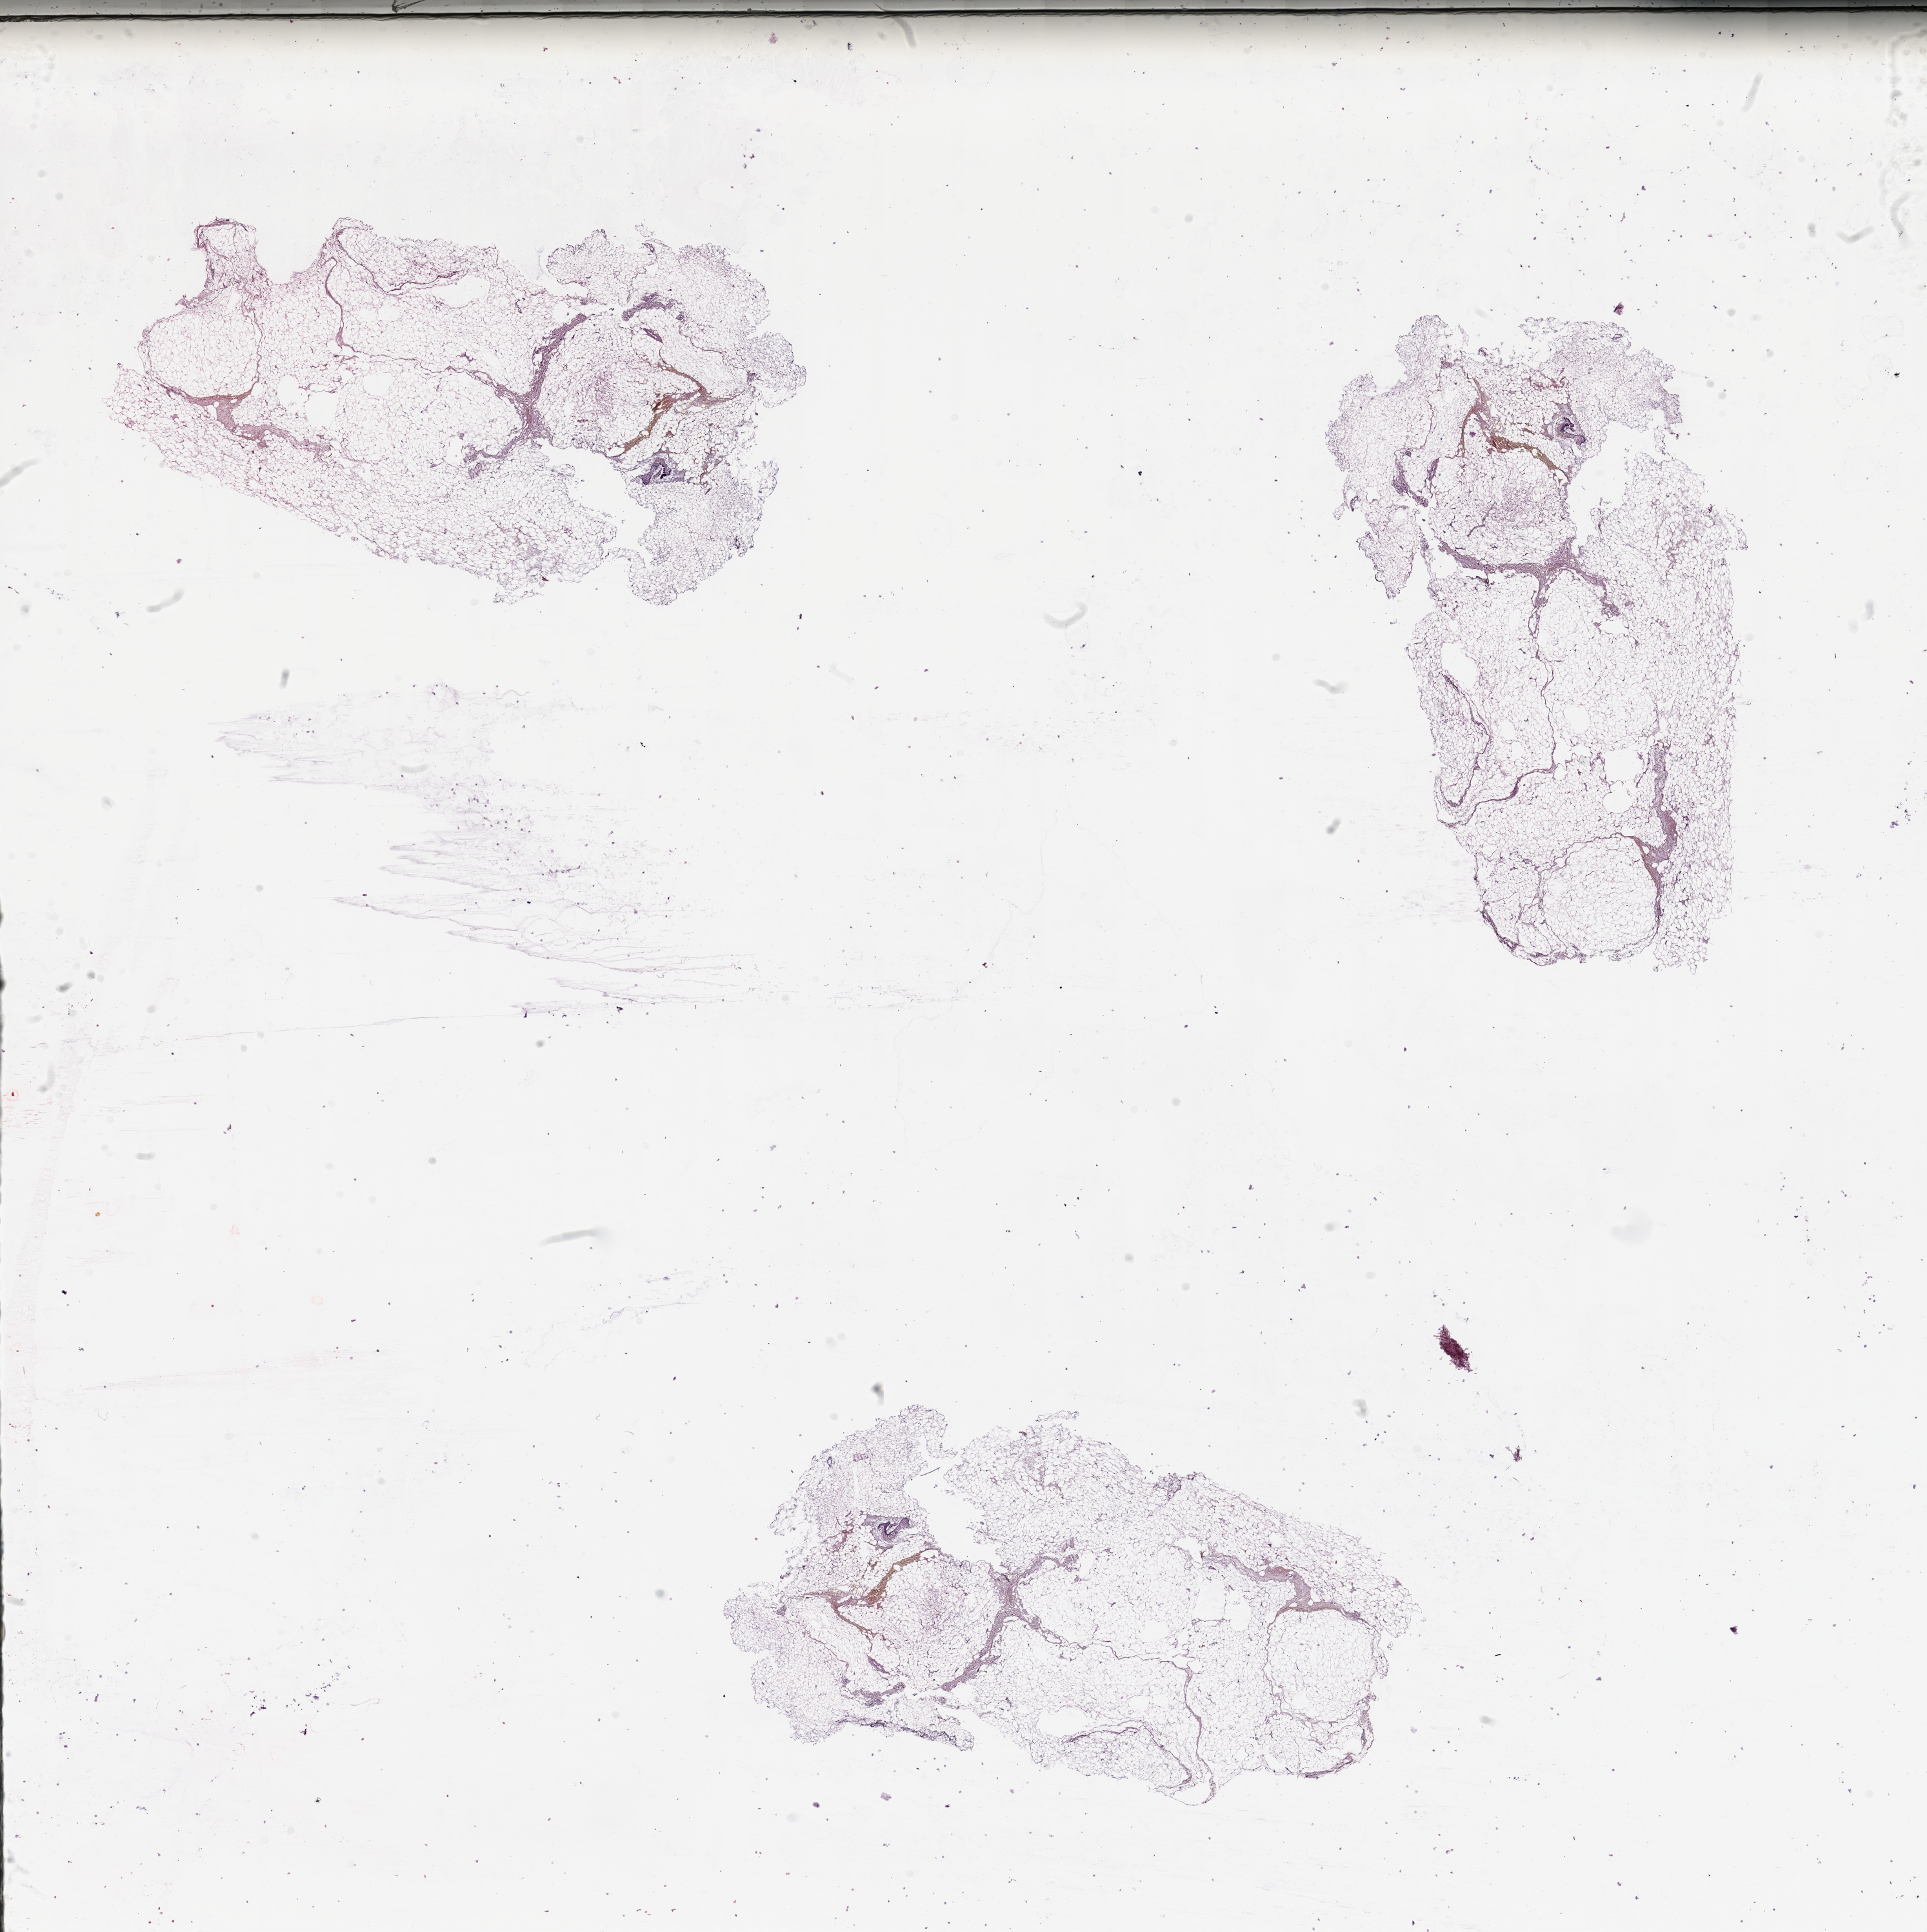
H&E whole-slide image, a low-resolution overview of the entire scanned area, about 23.6 x 23.7 mm, normal (non-tumour) tissue sample, sampled site: trunk. Patient: female, age 51 years.
This section: normal (non-tumour) tissue from the same patient. Patient diagnosis: Malignant melanoma, NOS.